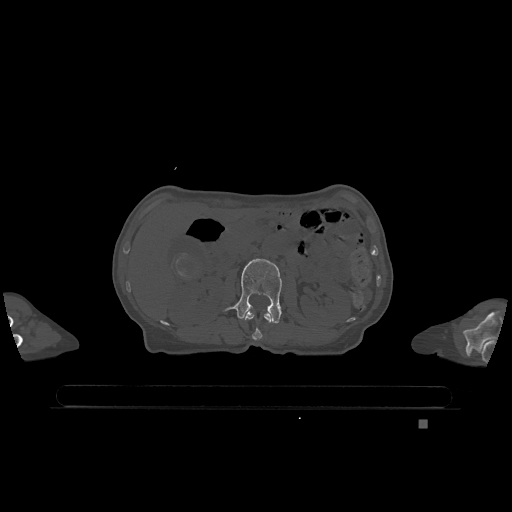
CT including the spine, one axial slice. Slice 431 of 1317 in the series (ordered by position). Bone window (W 1800 / L 400 HU). 0.5 mm slice thickness. 512 × 512 image matrix, field of view 500 × 500 mm. Patient: female, 74 years. From the clinical record (not read from this slice): primary cancer: lung; vertebrae with lytic lesions (as recorded): T1, T4, T5, T6, L4, L5.
Annotated regions visible in this slice (semi-automatically segmented with operator editing):
- L1 vertebra: bounding box <243,311,272,341> (left, top, right, bottom; pixels)
- L2 vertebra: <225,258,282,323>